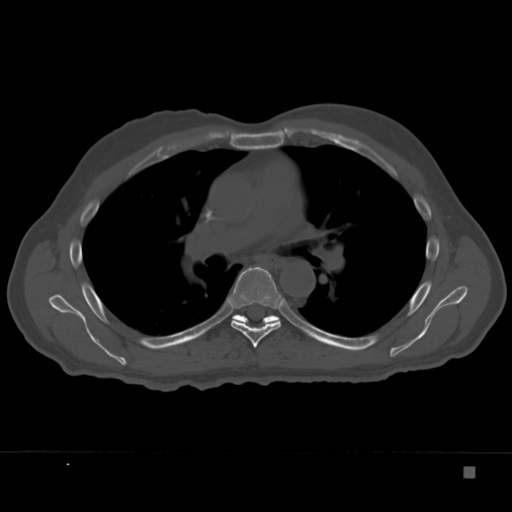
CT including the spine, one axial slice. Position 236 of 332 along the scan axis. Reconstruction kernel Br40s. Bone window (W 1800 / L 400 HU). 512 × 512 image matrix, field of view 389 × 389 mm. Patient: male, 72 years. From the clinical record (not read from this slice): primary cancer: skeletal.
Annotated regions visible in this slice (semi-automatic segmentation, software-assisted and operator-edited):
- T6 vertebra: bounding box <227,267,285,348> (left, top, right, bottom; pixels)
- T7 vertebra: <232,314,280,326>